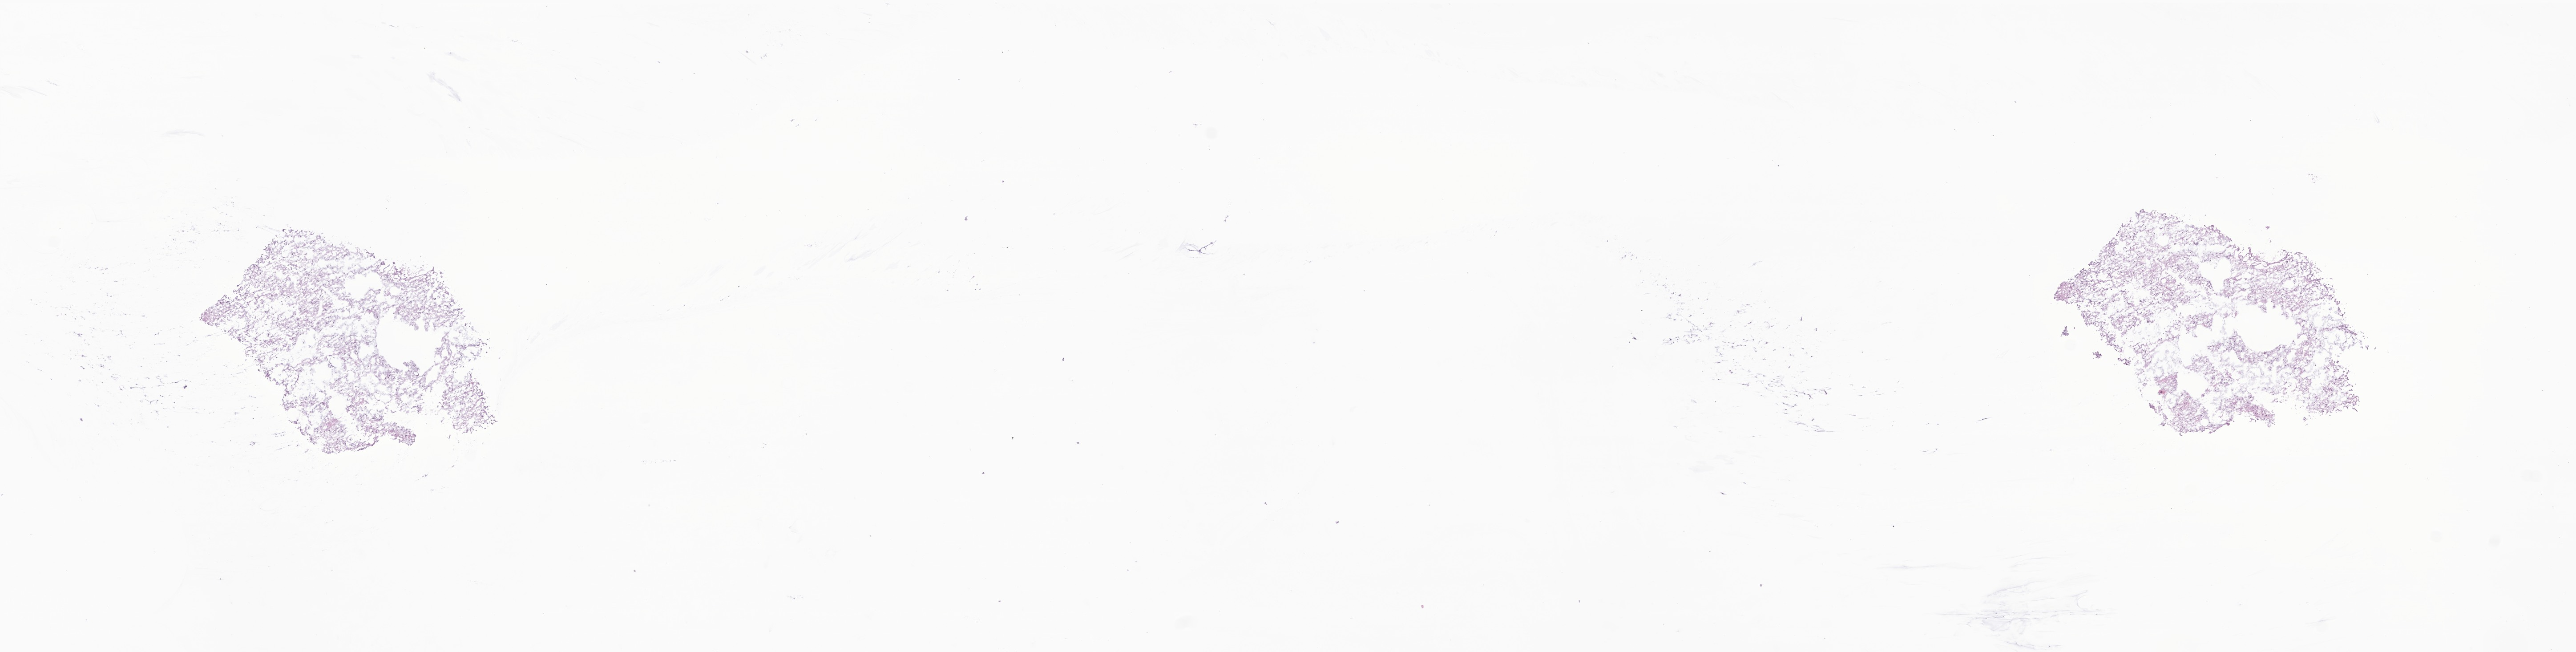
H&E whole-slide image of tumor tissue from the brain — low-resolution overview of the scanned area, about 24.4 x 6.2 mm. Frozen section (OCT-embedded). Patient: male, age 178 months (14 years 10 months).
Diagnosis (ICD-O-3 morphology term): Pilocytic astrocytoma.